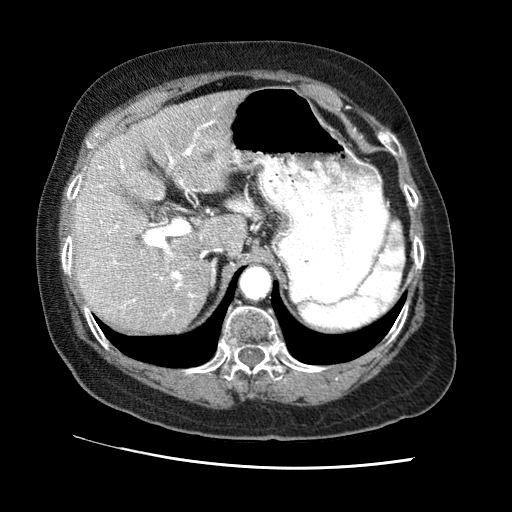
Contrast-enhanced abdominal CT (liver protocol), one axial slice; slice 43 of 65 in the series (ordered by position); soft-tissue window (W 400 / L 40 HU); 2.5 mm slice thickness; 512 × 512 image matrix, field of view 340 × 340 mm. Case-level facts recorded for this patient, not image findings: diagnosis: hepatocellular carcinoma (patient treated with transarterial chemoembolisation; whether this scan precedes or follows treatment is not stated here); TNM stage (as recorded): Stage-II; Child-Pugh class: A; tumour differentiation: no biopsy; tumour nodularity: multinodular.
Structures marked on this image (semi-automatic segmentation, software-assisted and operator-edited):
- liver parenchyma outside the tumour (the mass and vessels are separate outlines, so this box may not span the whole liver): box from (x=73, y=90) to (x=247, y=332) px
- liver vessels: (x=78, y=121)–(x=215, y=312)